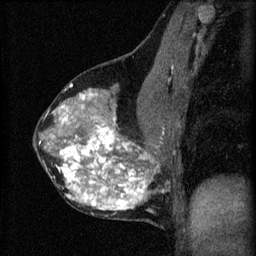
Breast MRI (dynamic contrast-enhanced), one sagittal slice. Position 33 of 60 along the scan axis. 3 images stored at this slice position (order not interpretable as contrast timing). 1.5 T. TE 4.2 ms, TR 8.2 ms. 2 mm slice thickness. 256 × 256 image matrix, field of view 180 × 180 mm. Patient: female, 40 years.
Outlined on this slice (semi-automatically segmented with operator editing):
- analysis volume of interest (the breast-tissue region the enhancement analysis was run in; not a lesion): bounding box (x1, y1, x2, y2) in pixels: (34, 76, 179, 219)
- tumour enhancement mask (voxels above the 70 % enhancement threshold inside the analysis volume of interest): (40, 84, 163, 211)